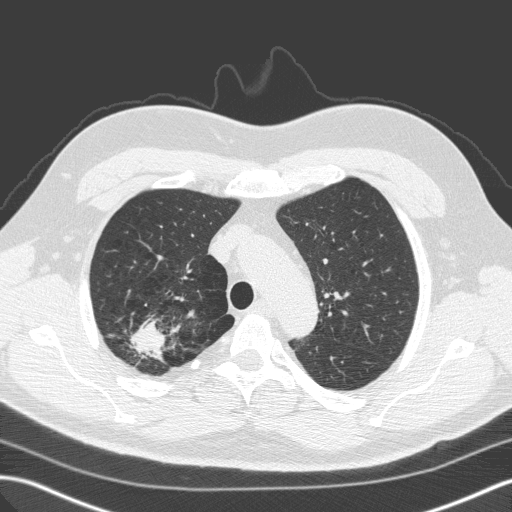
Axial slice from a low-dose chest CT screening exam; first (baseline) screen; lung window (W 1500 / L -600 HU); 2 mm slice thickness; standard (soft-tissue) reconstruction kernel (C); slice 32 of 149 in the series; 512 × 512 image matrix, field of view 357 × 357 mm. Male participant, aged 59 years at enrolment. Former smoker at enrolment.
Expert-annotated lung lesion, box from (x=117, y=310) to (x=178, y=371) px. Screening reader's record for this exam (one nodule recorded; not confirmed to be the boxed lesion): non-calcified nodule or mass ≥4 mm, right upper lobe, 28 × 25 mm, spiculated (stellate) margins, soft tissue attenuation. Official screen result: positive, change unspecified: nodule(s) >= 4 mm or enlarging nodule(s), mass(es), or other non-specific abnormalities suspicious for lung cancer. Participant outcome: lung cancer diagnosed 64 days after this screen — large cell carcinoma, NOS, right upper lobe, undifferentiated (G4), stage IA (AJCC 6th edition), 25 mm at pathology.